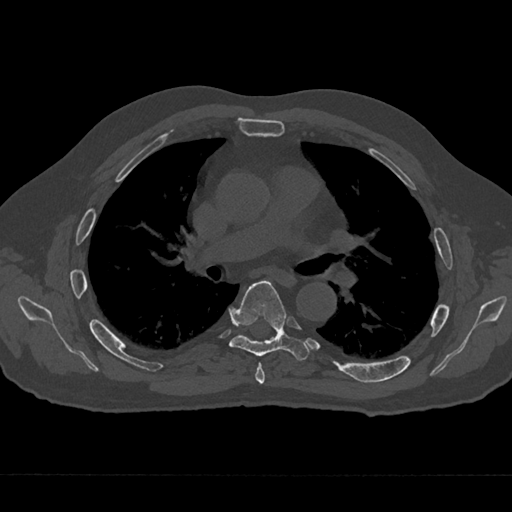
CT including the spine, one axial slice; position 425 of 797 along the scan axis; 120 kVp; bone window (W 1800 / L 400 HU); 0.5 mm slice thickness; 512 × 512 image matrix. Patient: male, 75 years. Case-level facts recorded for this patient, not image findings: primary cancer: renal; vertebrae with lytic lesions (as recorded): T4.
Structures marked on this image (semi-automatic segmentation, software-assisted and operator-edited):
- T5 vertebra: box from (x=255, y=362) to (x=265, y=385) px
- T6 vertebra: (x=229, y=281)–(x=309, y=361)